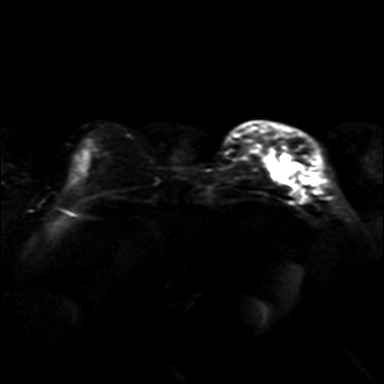
Breast MRI, one axial slice. Diffusion-weighted series; image 2 of 4 stored at this slice position (different b-values; order by instance number). 3 T. 384 × 384 image matrix, field of view 320 × 320 mm. Female patient.
Outlined on this slice (outlined manually by an expert reader):
- tumour on diffusion-weighted imaging: box from (x=270, y=153) to (x=291, y=179) px